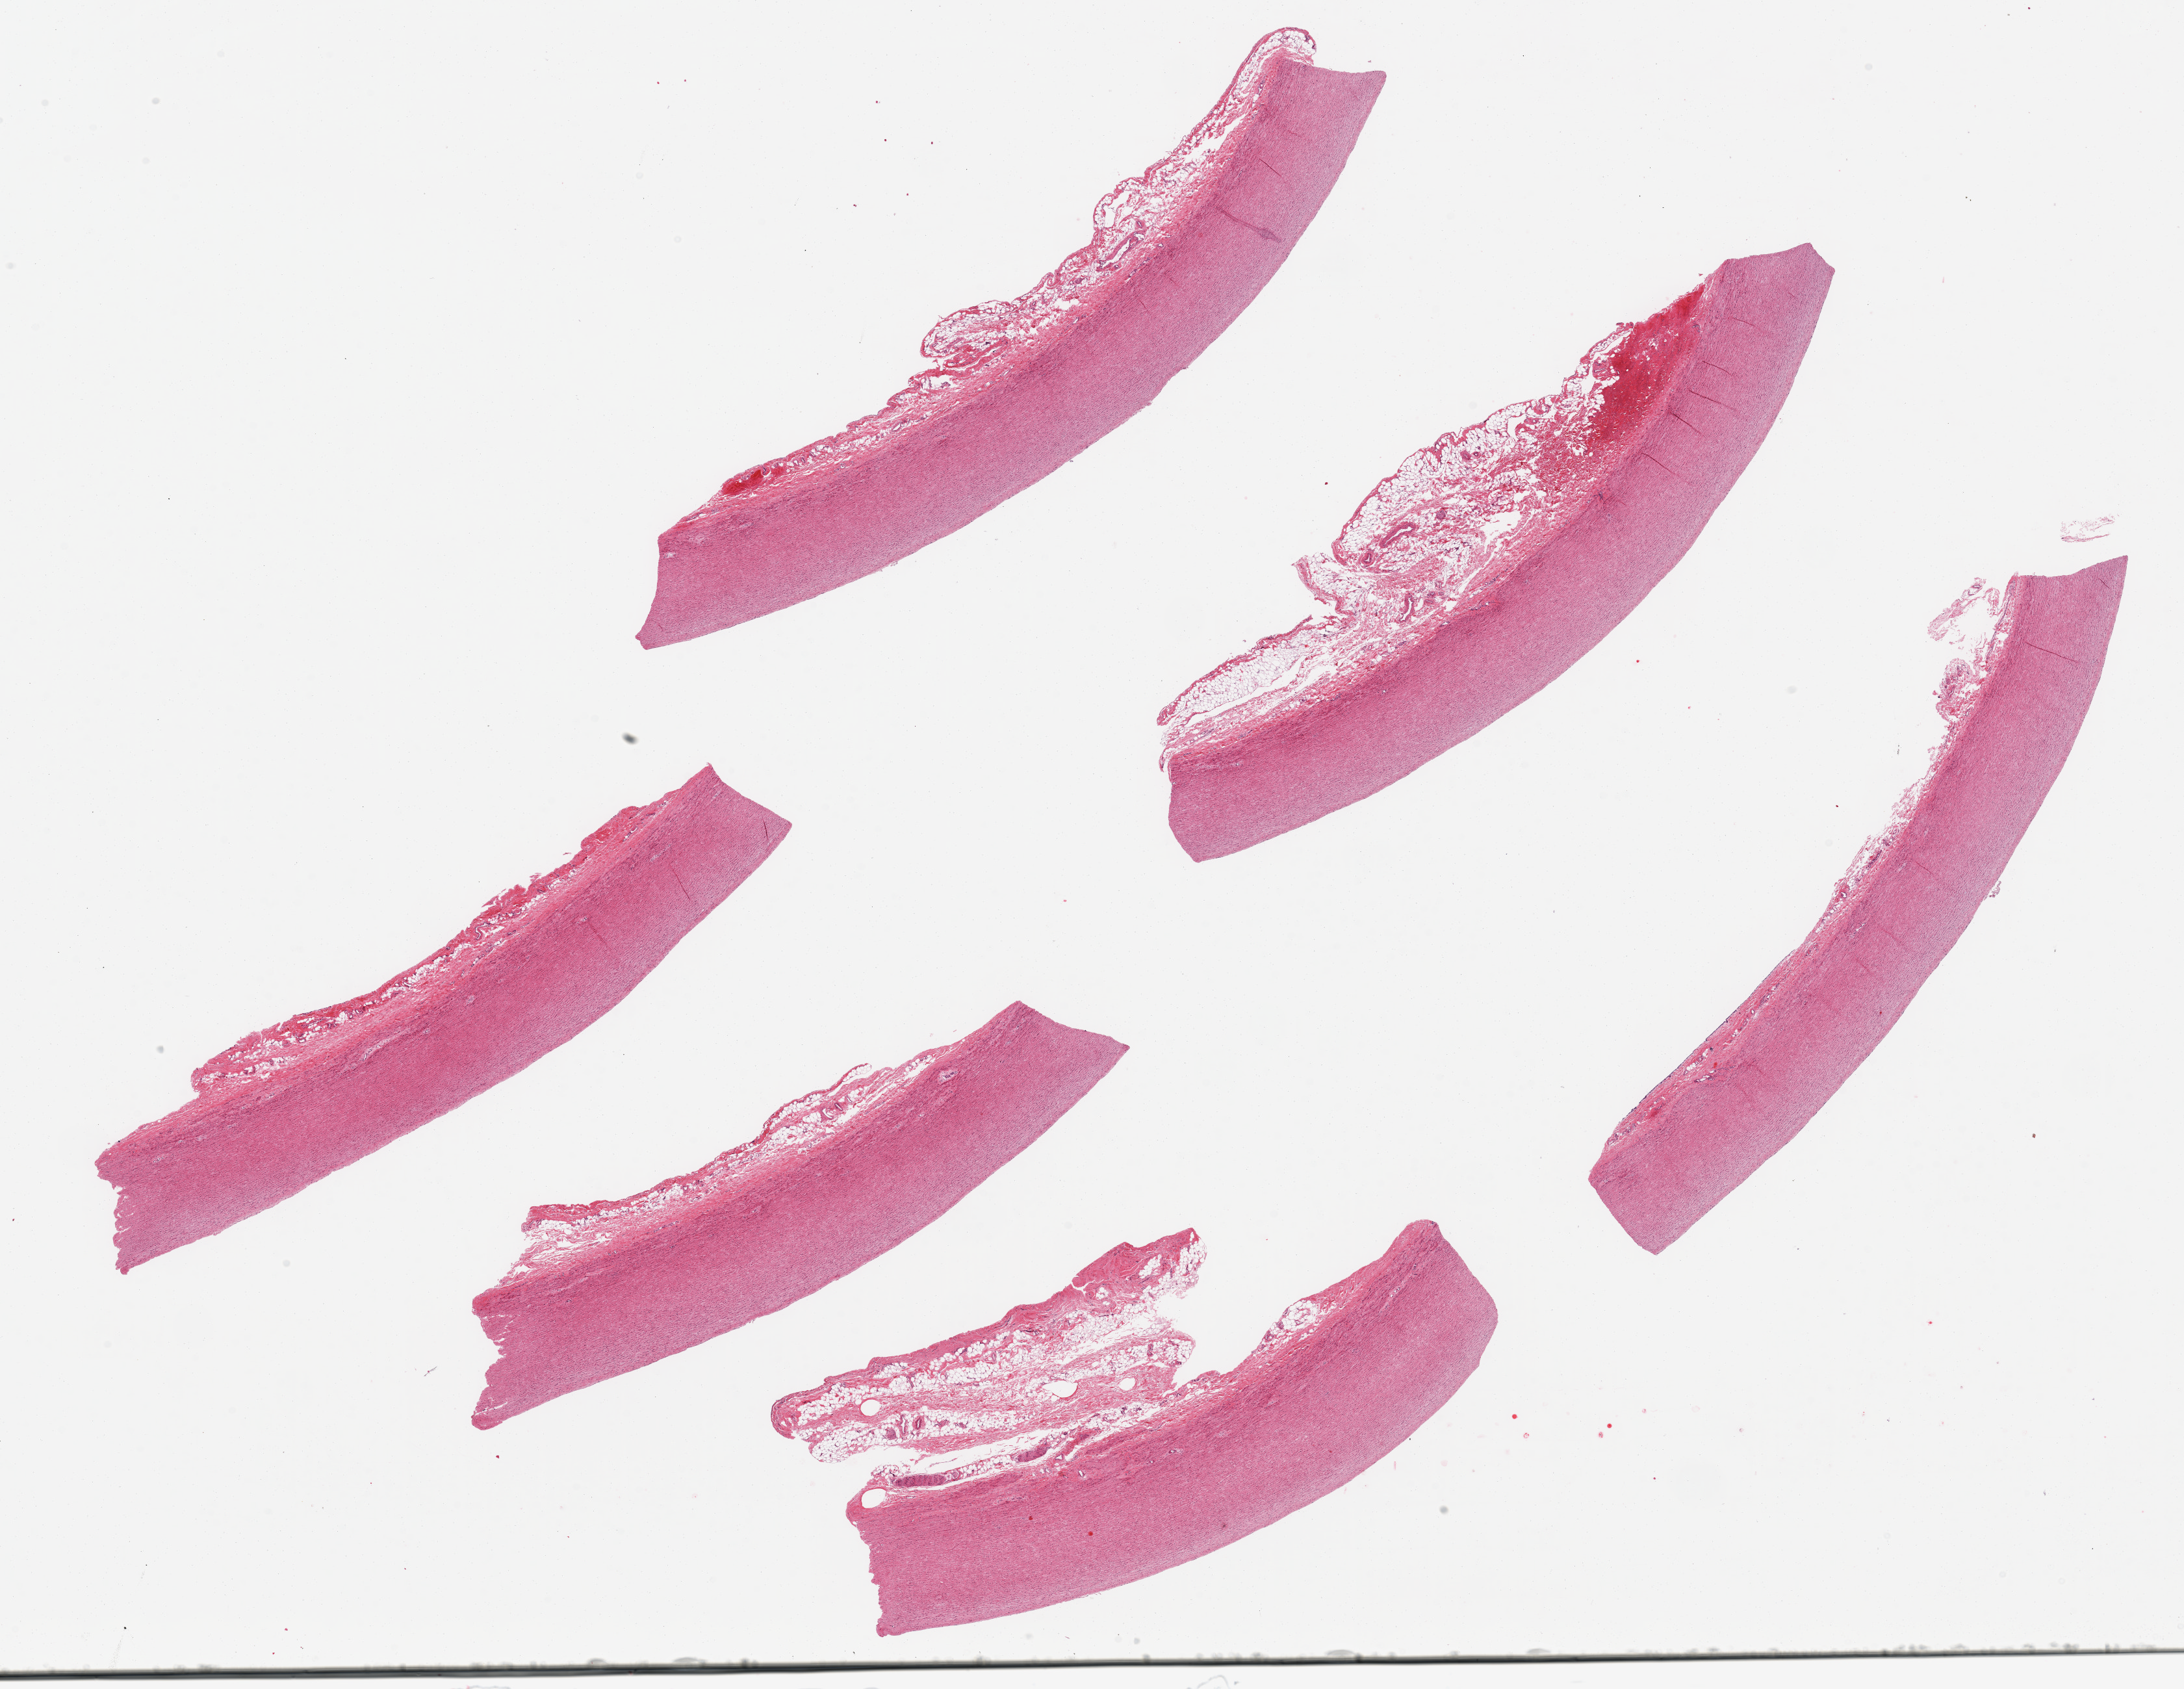
Whole-slide image, H&E stain, brightfield, a low-resolution overview of the entire scanned area, about 26.6 x 20.6 mm (acquisition: 20x scan); PAXgene-fixed, paraffin-embedded tissue; section of aorta (target tissue); tissue donor sample. Donor: male.
• pathologist's review note for this sample: 6 pieces, up to 11x3 mm; no plaques; 2 pieces have about 40% periaortic adipose tissue